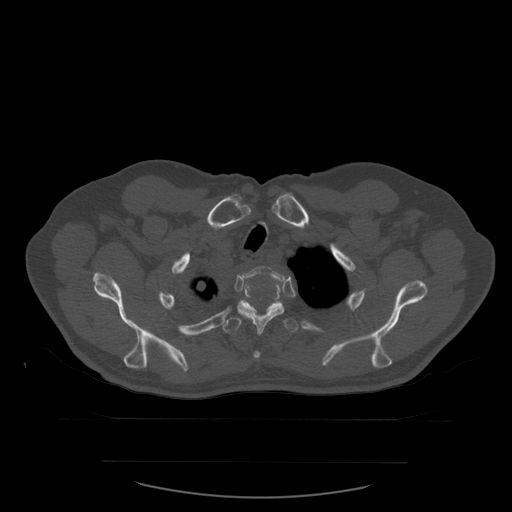
CT including the spine, one axial slice. Slice 456 of 590 in the series (ordered by position). Bone window (W 1800 / L 400 HU). 1.25 mm slice thickness. 512 × 512 image matrix, field of view 479 × 479 mm. Patient age 71 years. Case-level facts recorded for this patient, not image findings: primary cancer: lung; vertebrae with lytic lesions (as recorded): T1, T2, L5, S1.
Outlined on this slice (semi-automatic segmentation, software-assisted and operator-edited):
- T2 vertebra: bounding box [x1, y1, x2, y2] px = [243, 266, 284, 281]
- T3 vertebra: [237, 285, 285, 358]
- T4 vertebra: [222, 298, 299, 334]